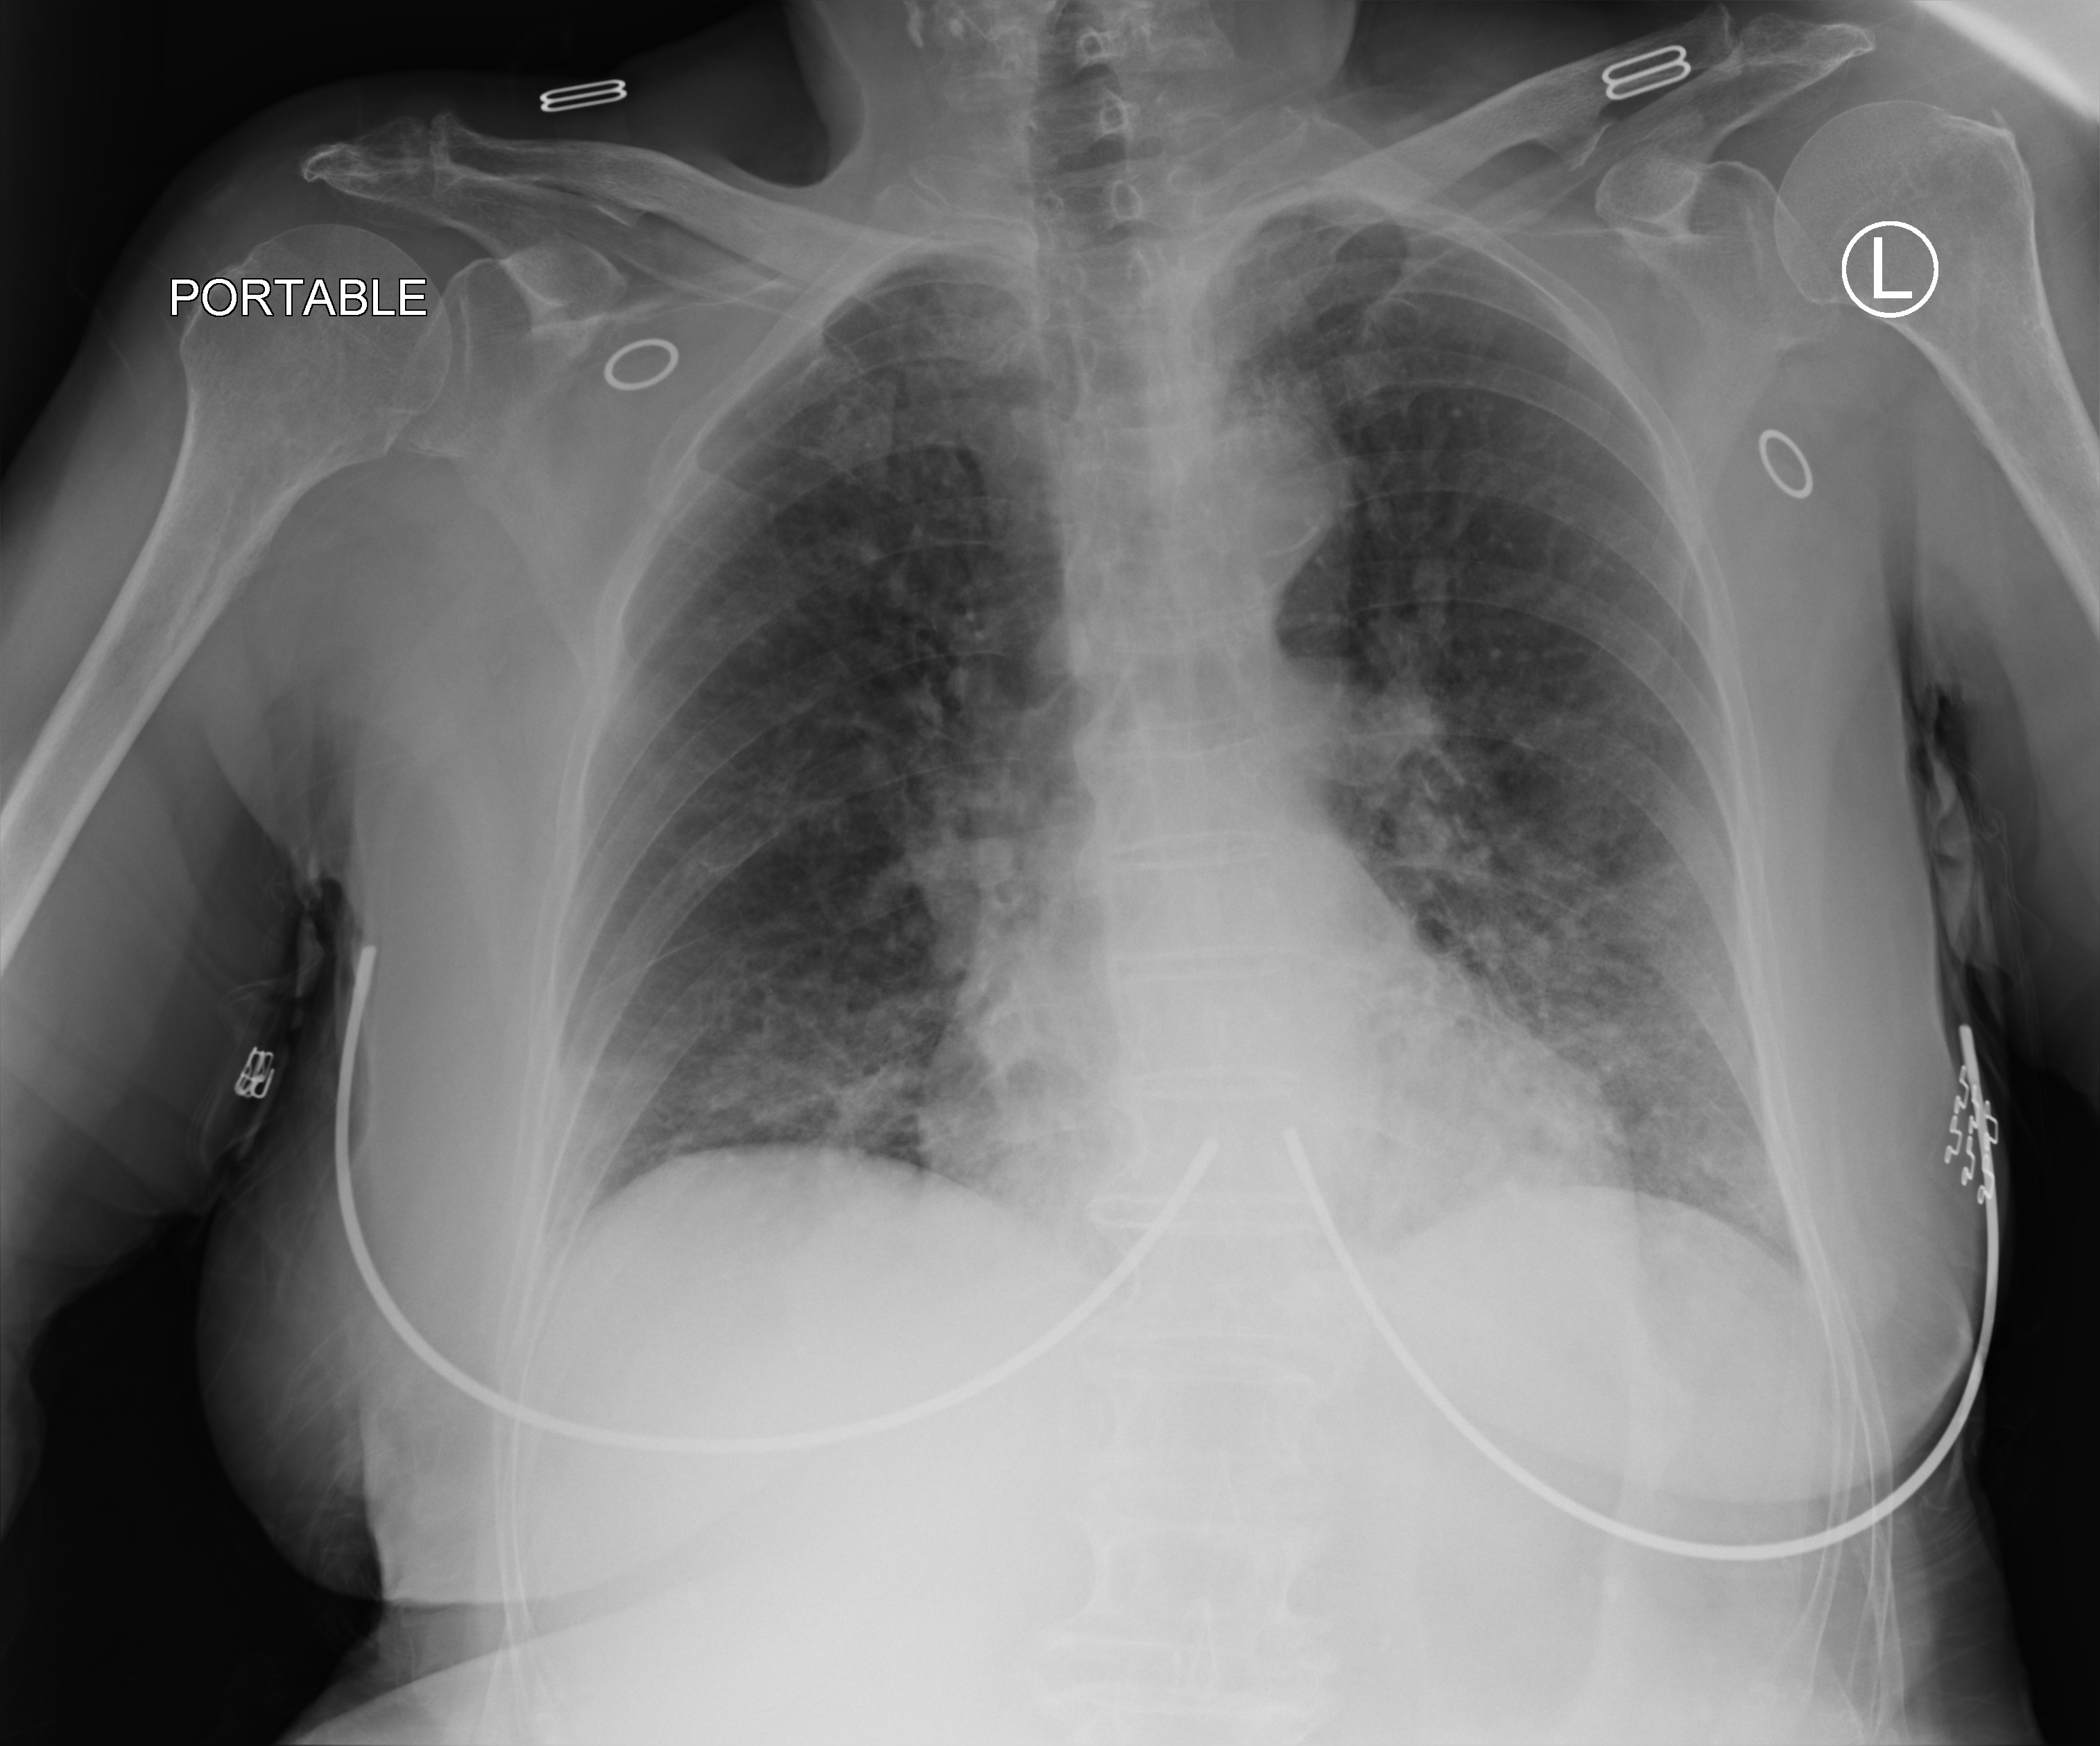
Portable chest radiograph; anteroposterior (AP) projection. Patient hospitalised with COVID-19; female, aged 75–90 years.
From the hospital-stay record, not from the radiograph (when in the stay this image was taken is not recorded): admitted to intensive care during this hospital stay: no; smoking status (admission record): never; other chronic lung disease (admission record): no.